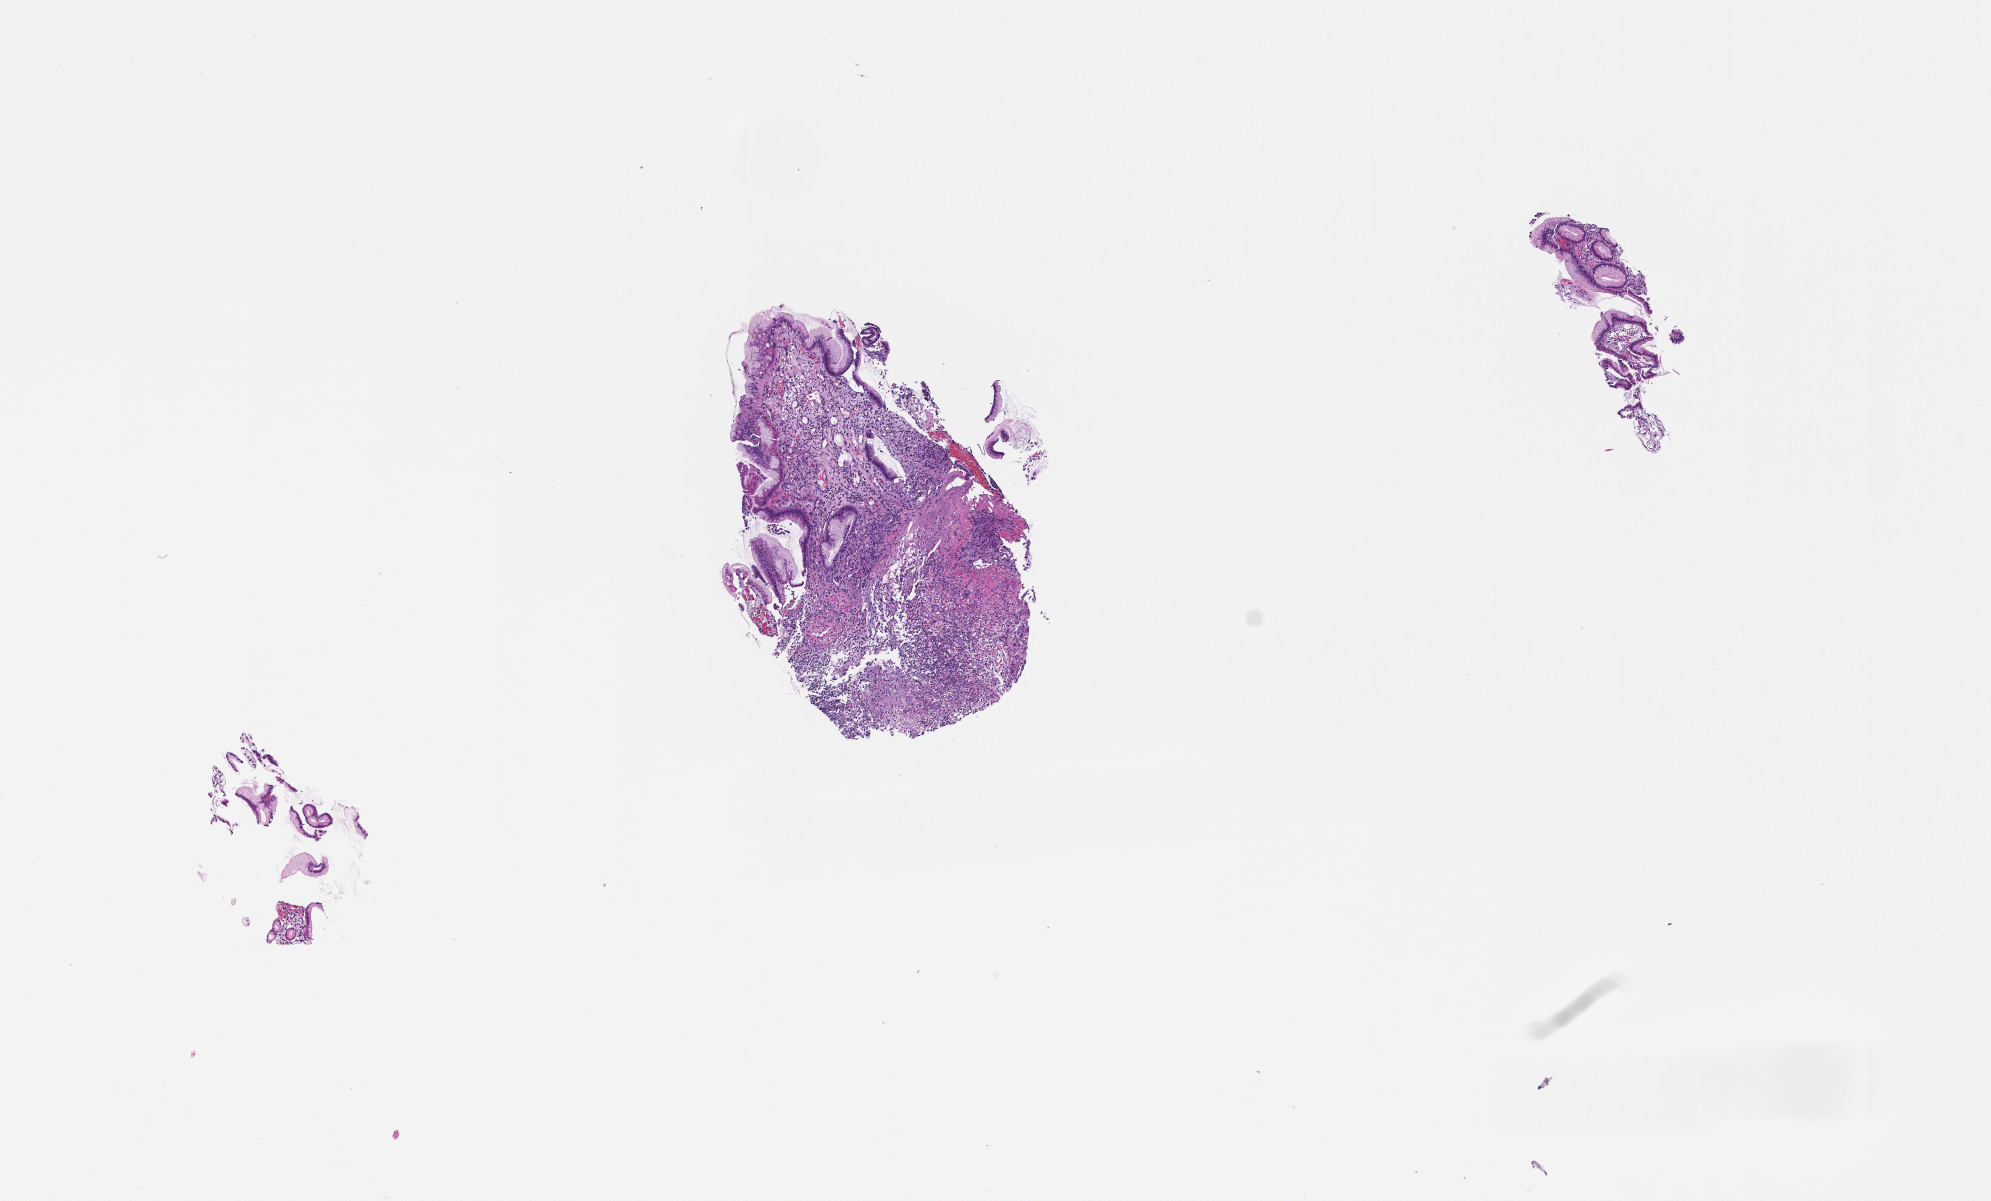
H&E whole-slide image — whole scanned area (about 8.0 x 4.9 mm) shown as a low-resolution overview; FFPE section; tissue site: stomach. Patient: female.
This section: primary tumor. Diagnosis: Adenocarcinoma of the Gastroesophageal Junction.